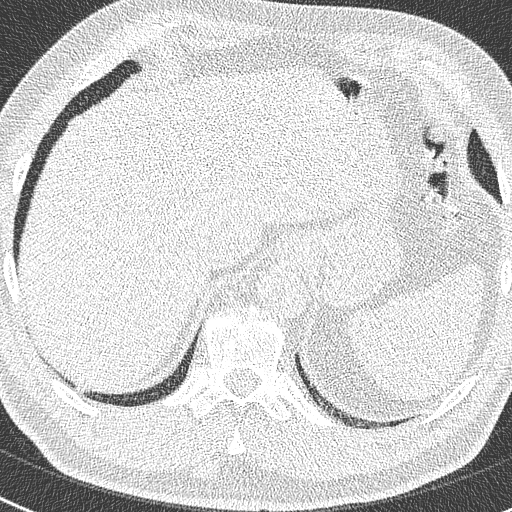
Low-dose screening chest CT, axial slice, second annual screen, lung window (W 1500 / L -600 HU), 2 mm slice thickness. Male participant, aged 63 years at enrolment. Former smoker at enrolment.
Expert-annotated lung lesion, bounding box [x1, y1, x2, y2] px = [64, 375, 97, 404]. No non-calcified nodule or mass ≥4 mm was recorded by the screening reader at this exam. Official screen result: negative screen, no significant abnormalities. Lung cancer was diagnosed 262 days after this screen: adenocarcinoma, NOS, right lower lobe, moderately differentiated (G2), stage IIIB (AJCC 6th edition), 17 mm at pathology.